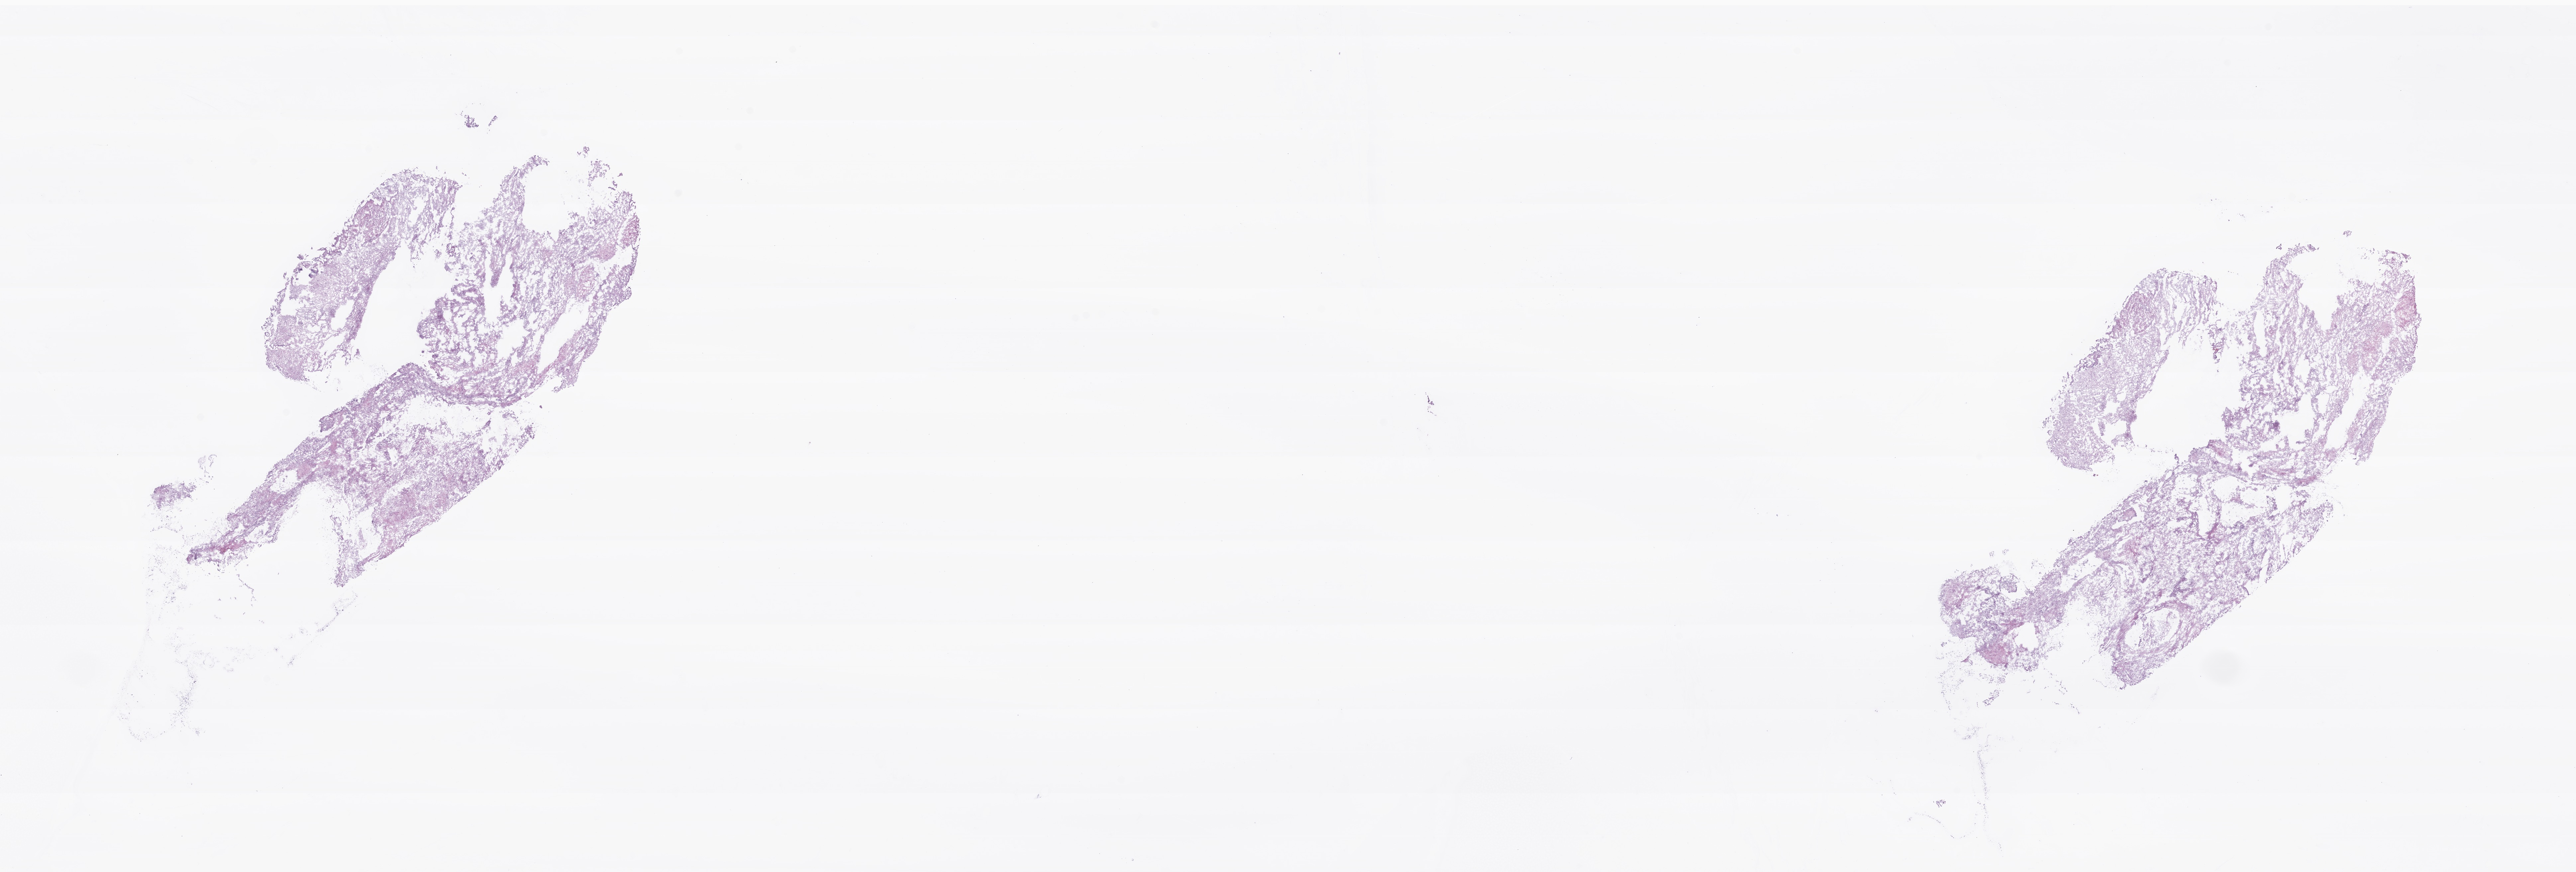
Whole-slide image, H&E stain of tumor tissue from the brain, low-resolution overview of the scanned area, about 32.6 x 11.0 mm, frozen section (OCT-embedded). Female patient, age 158 months (13 years 2 months).
Recorded diagnosis: Pilocytic astrocytoma.